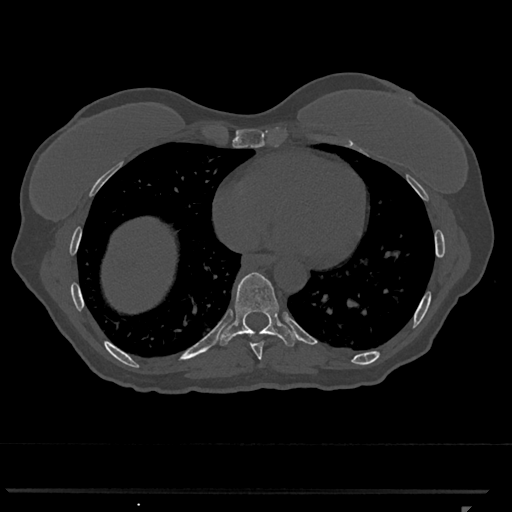
CT including the spine, one axial slice; slice 632 of 793 in the series (ordered by position); reconstruction kernel Br40s/3; 120 kVp; bone window (W 1800 / L 400 HU); 0.5 mm slice thickness; 512 × 512 image matrix. Female patient, age 62 years. From the clinical record (not read from this slice): primary cancer: renal.
Structures marked on this image (semi-automatic segmentation, software-assisted and operator-edited):
- T8 vertebra: bounding box <250,341,264,360> (left, top, right, bottom; pixels)
- T9 vertebra: <220,272,298,346>